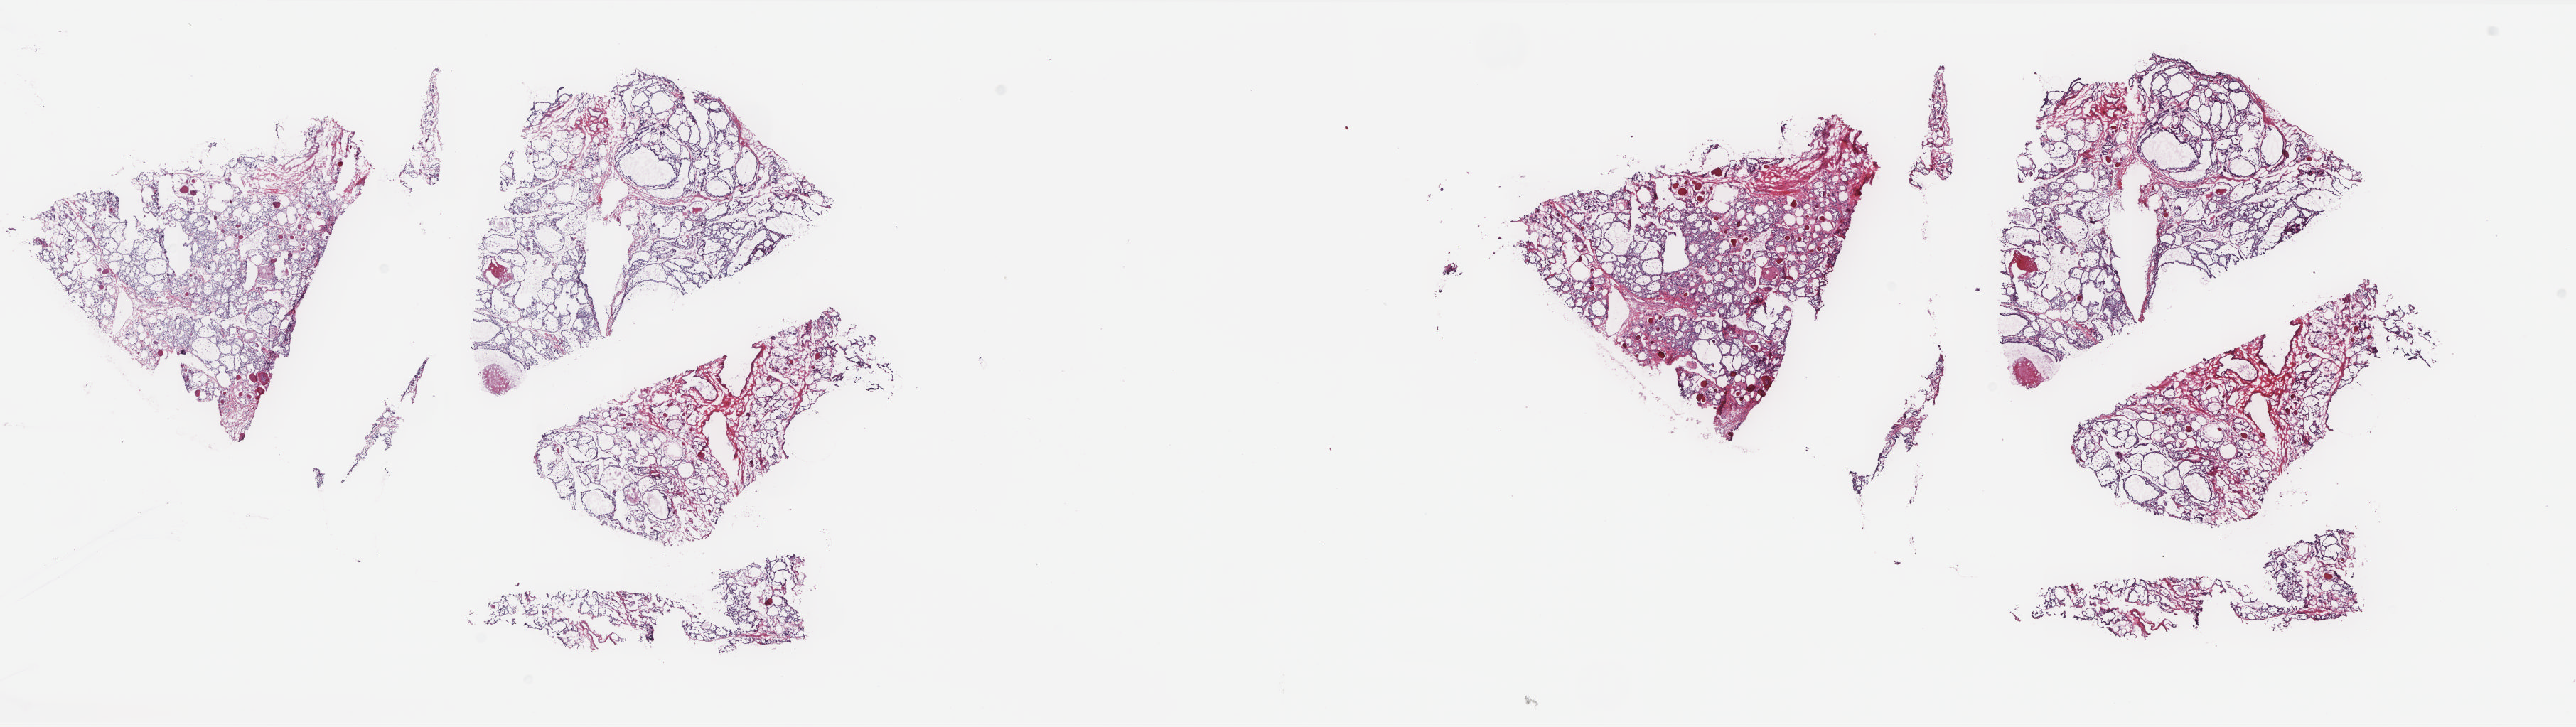
H&E-stained whole-slide image, whole scanned area (about 28.9 x 8.2 mm) shown as a low-resolution overview; frozen section; solid tissue normal (non-tumour tissue) sample from the thyroid. Female, age 68 years at initial diagnosis. Composition of this section per pathologist review: tumour cells 0%, tumour nuclei 0%, normal cells 100%, stromal cells 0%, necrosis 0%. Infiltration values recorded for this section: lymphocyte infiltration 0%, monocyte infiltration 0%, neutrophil infiltration 0%.
This section: solid tissue normal sample (biorepository sample class). Patient diagnosis: Papillary carcinoma, follicular variant.